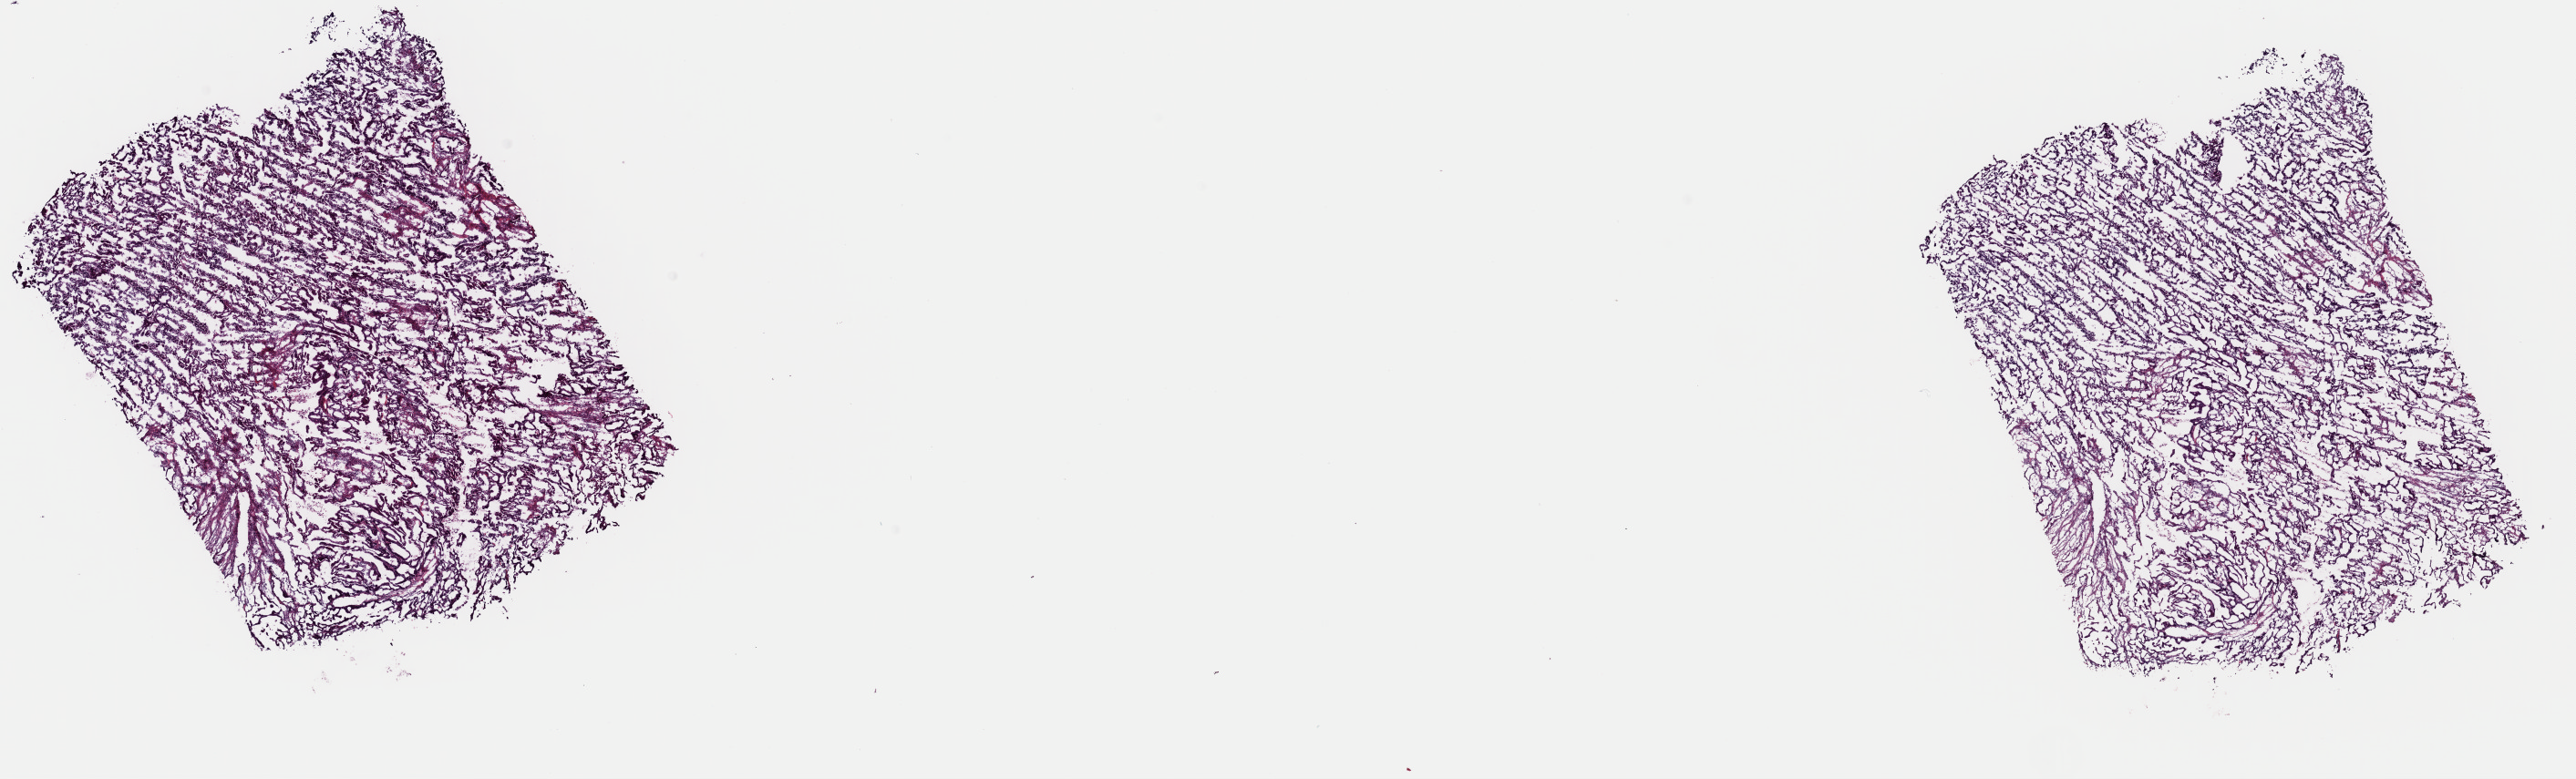
Whole-slide histology image, H&E — low-resolution overview of the scanned area, about 22.3 x 6.8 mm; frozen section from the top of the tissue portion; primary tumour sample from the cervix. Female, age 53 years at initial diagnosis. Histologic grade: G3 (poorly differentiated). Pathologist review of this section (percent, as recorded): tumour cells 99%, tumour nuclei 90%, normal cells 0%, stromal cells 0%, necrosis 1%. Infiltration values recorded for this section: lymphocyte infiltration 1%, monocyte infiltration 0%, neutrophil infiltration 0%.
Diagnosis: Adenocarcinoma, endocervical type. Lymph nodes positive (case pathology): 0 of 29 examined. FIGO stage: IB1.